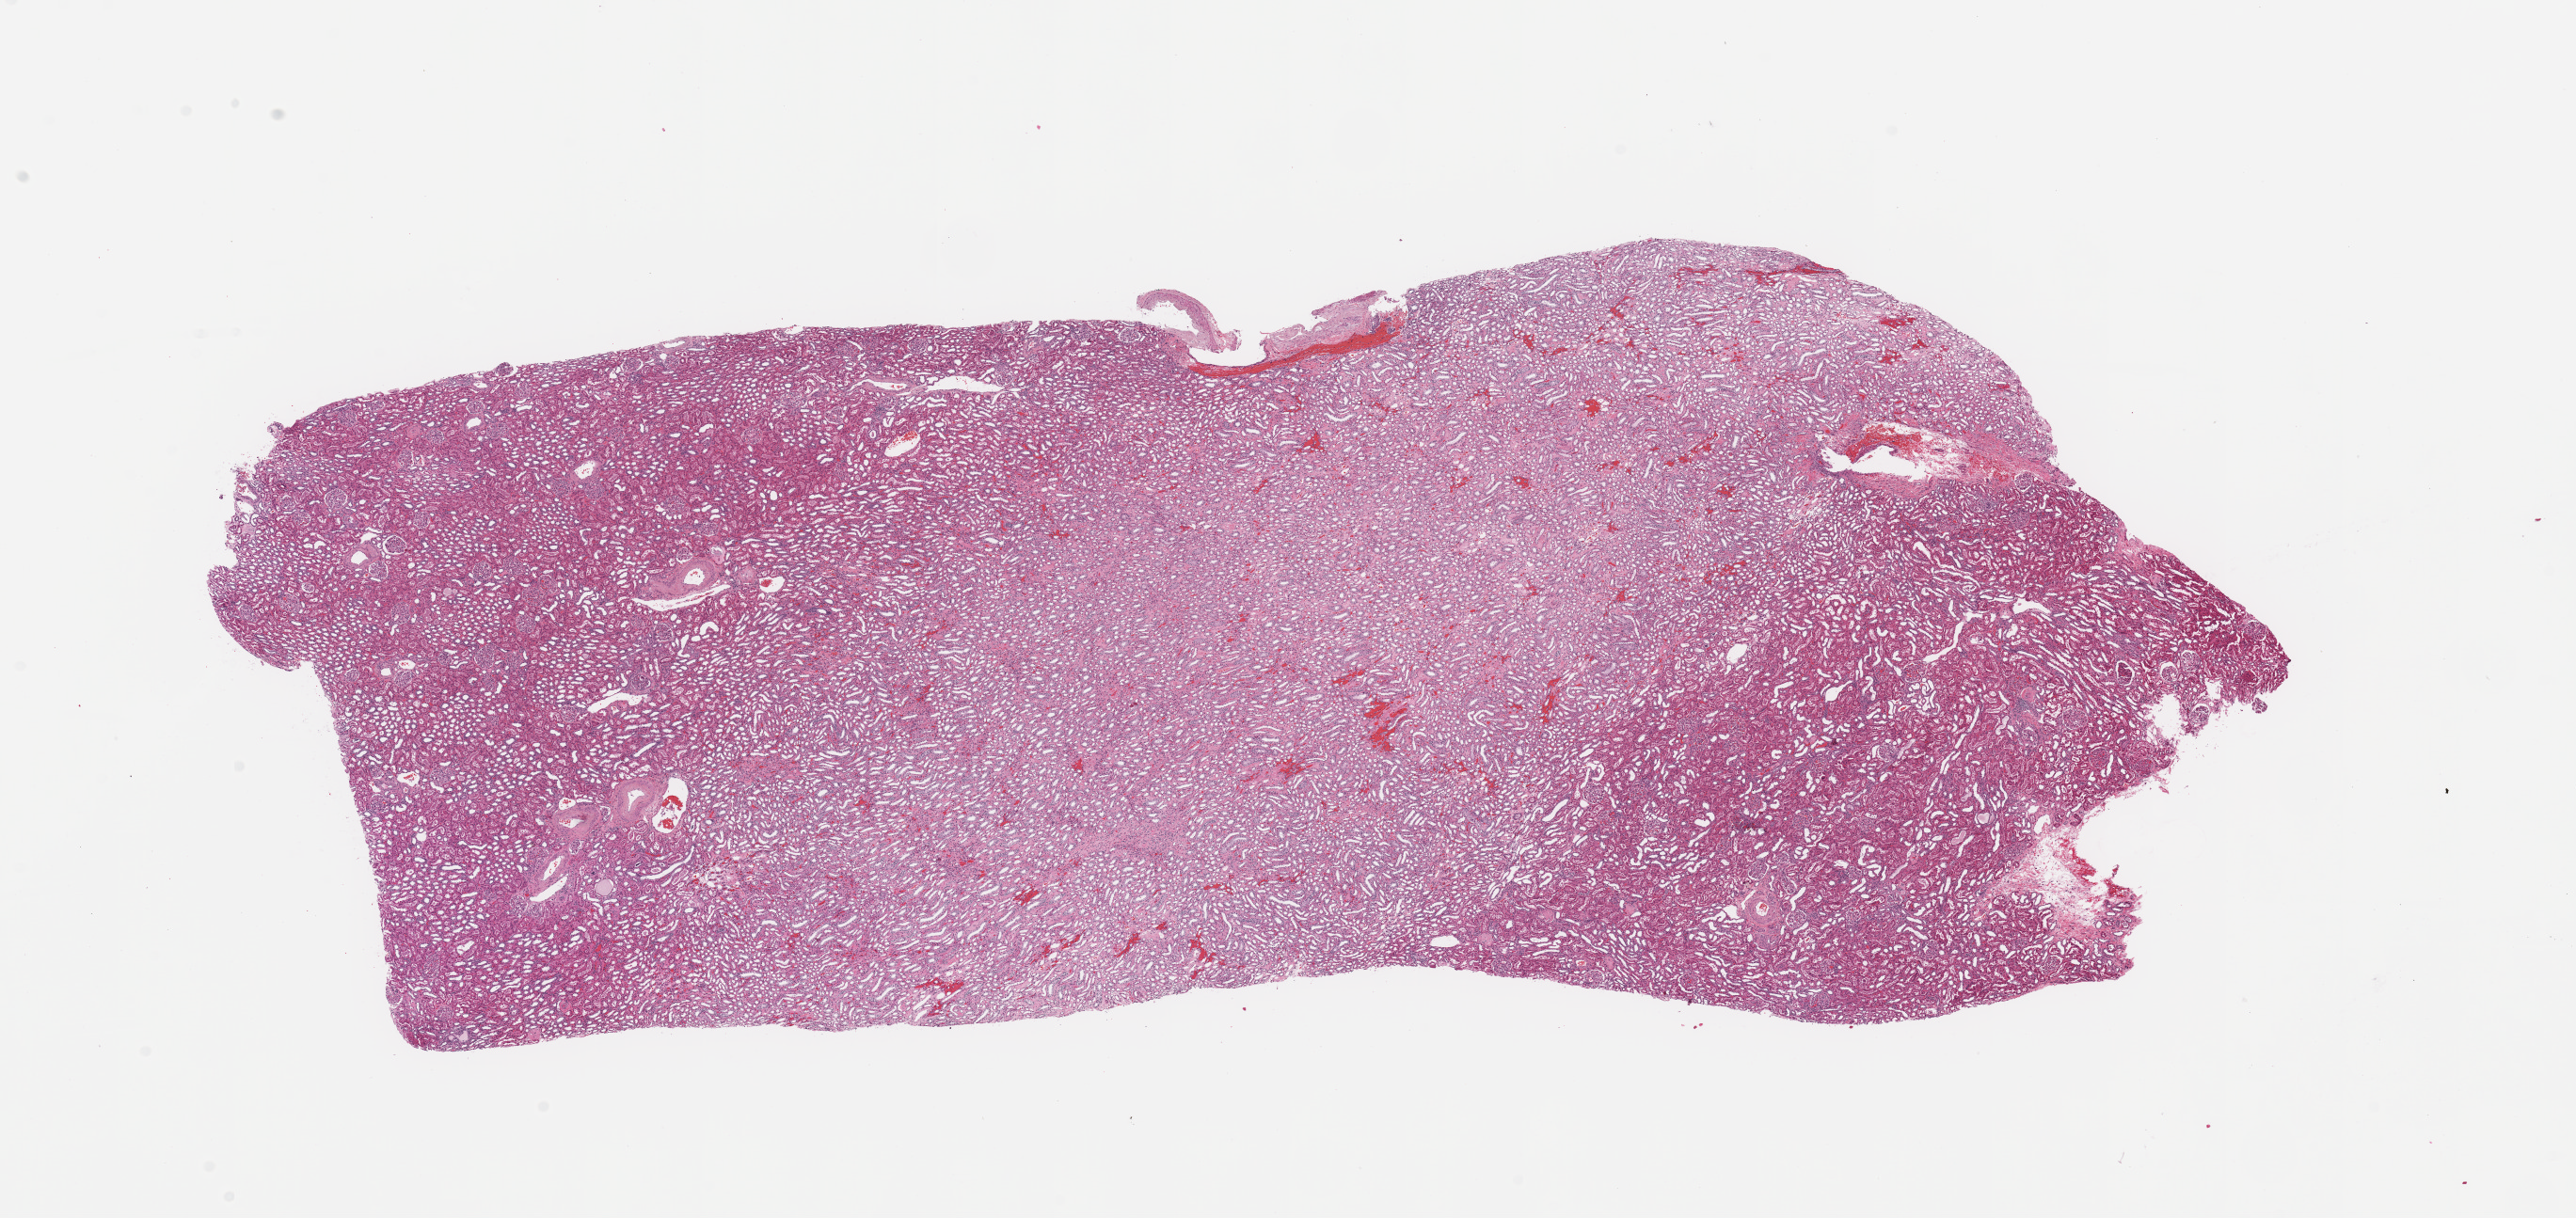
Digitized Hematoxylin and eosin (H&E) stained tissue section (whole slide) — a low-resolution overview of the entire scanned area, about 21.7 x 10.2 mm (acquisition: 20x scan); normal (non-tumour) tissue sample, sampled site: kidney. Female, 59 y/o.
This section: normal (non-tumour) tissue from the same patient. Patient diagnosis: Renal cell carcinoma, NOS.